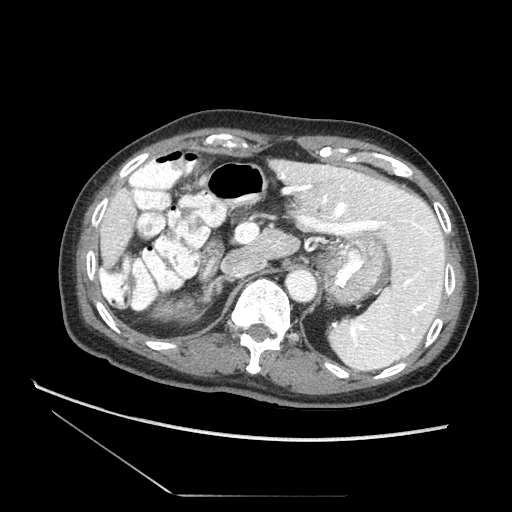
Contrast-enhanced abdominal CT (liver protocol), one axial slice; slice 50 of 73 in the series (ordered by position); reconstruction kernel STANDARD; soft-tissue window (W 400 / L 40 HU); 2.5 mm slice thickness; 512 × 512 image matrix. Case-level facts recorded for this patient, not image findings: diagnosis: hepatocellular carcinoma (patient treated with transarterial chemoembolisation; whether this scan precedes or follows treatment is not stated here); TNM stage (as recorded): Stage-II; Child-Pugh class: A; tumour nodularity: multinodular.
Outlined on this slice (semi-automatically segmented with operator editing):
- liver parenchyma outside the tumour (the mass and vessels are separate outlines, so this box may not span the whole liver): bounding box (x1, y1, x2, y2) in pixels: (101, 160, 447, 354)
- liver vessels: (288, 183, 414, 255)